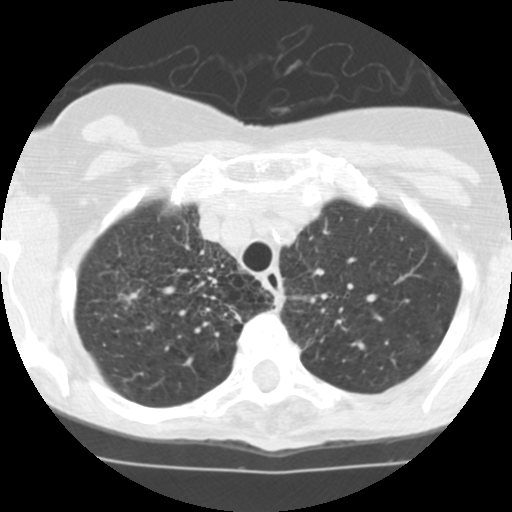
Low-dose screening chest CT, one axial slice. Slice 93 of 115 in the series (ordered by position). Reconstruction kernel STANDARD. 120 kVp. Lung window (W 1500 / L -600 HU). 2.5 mm slice thickness. 512 × 512 image matrix, field of view 280 × 280 mm.
Outlined on this slice (outlined manually by an expert reader):
- lesion 1 (tumor, upper lobe of right lung): bounding box <123,291,139,303> (left, top, right, bottom; pixels)